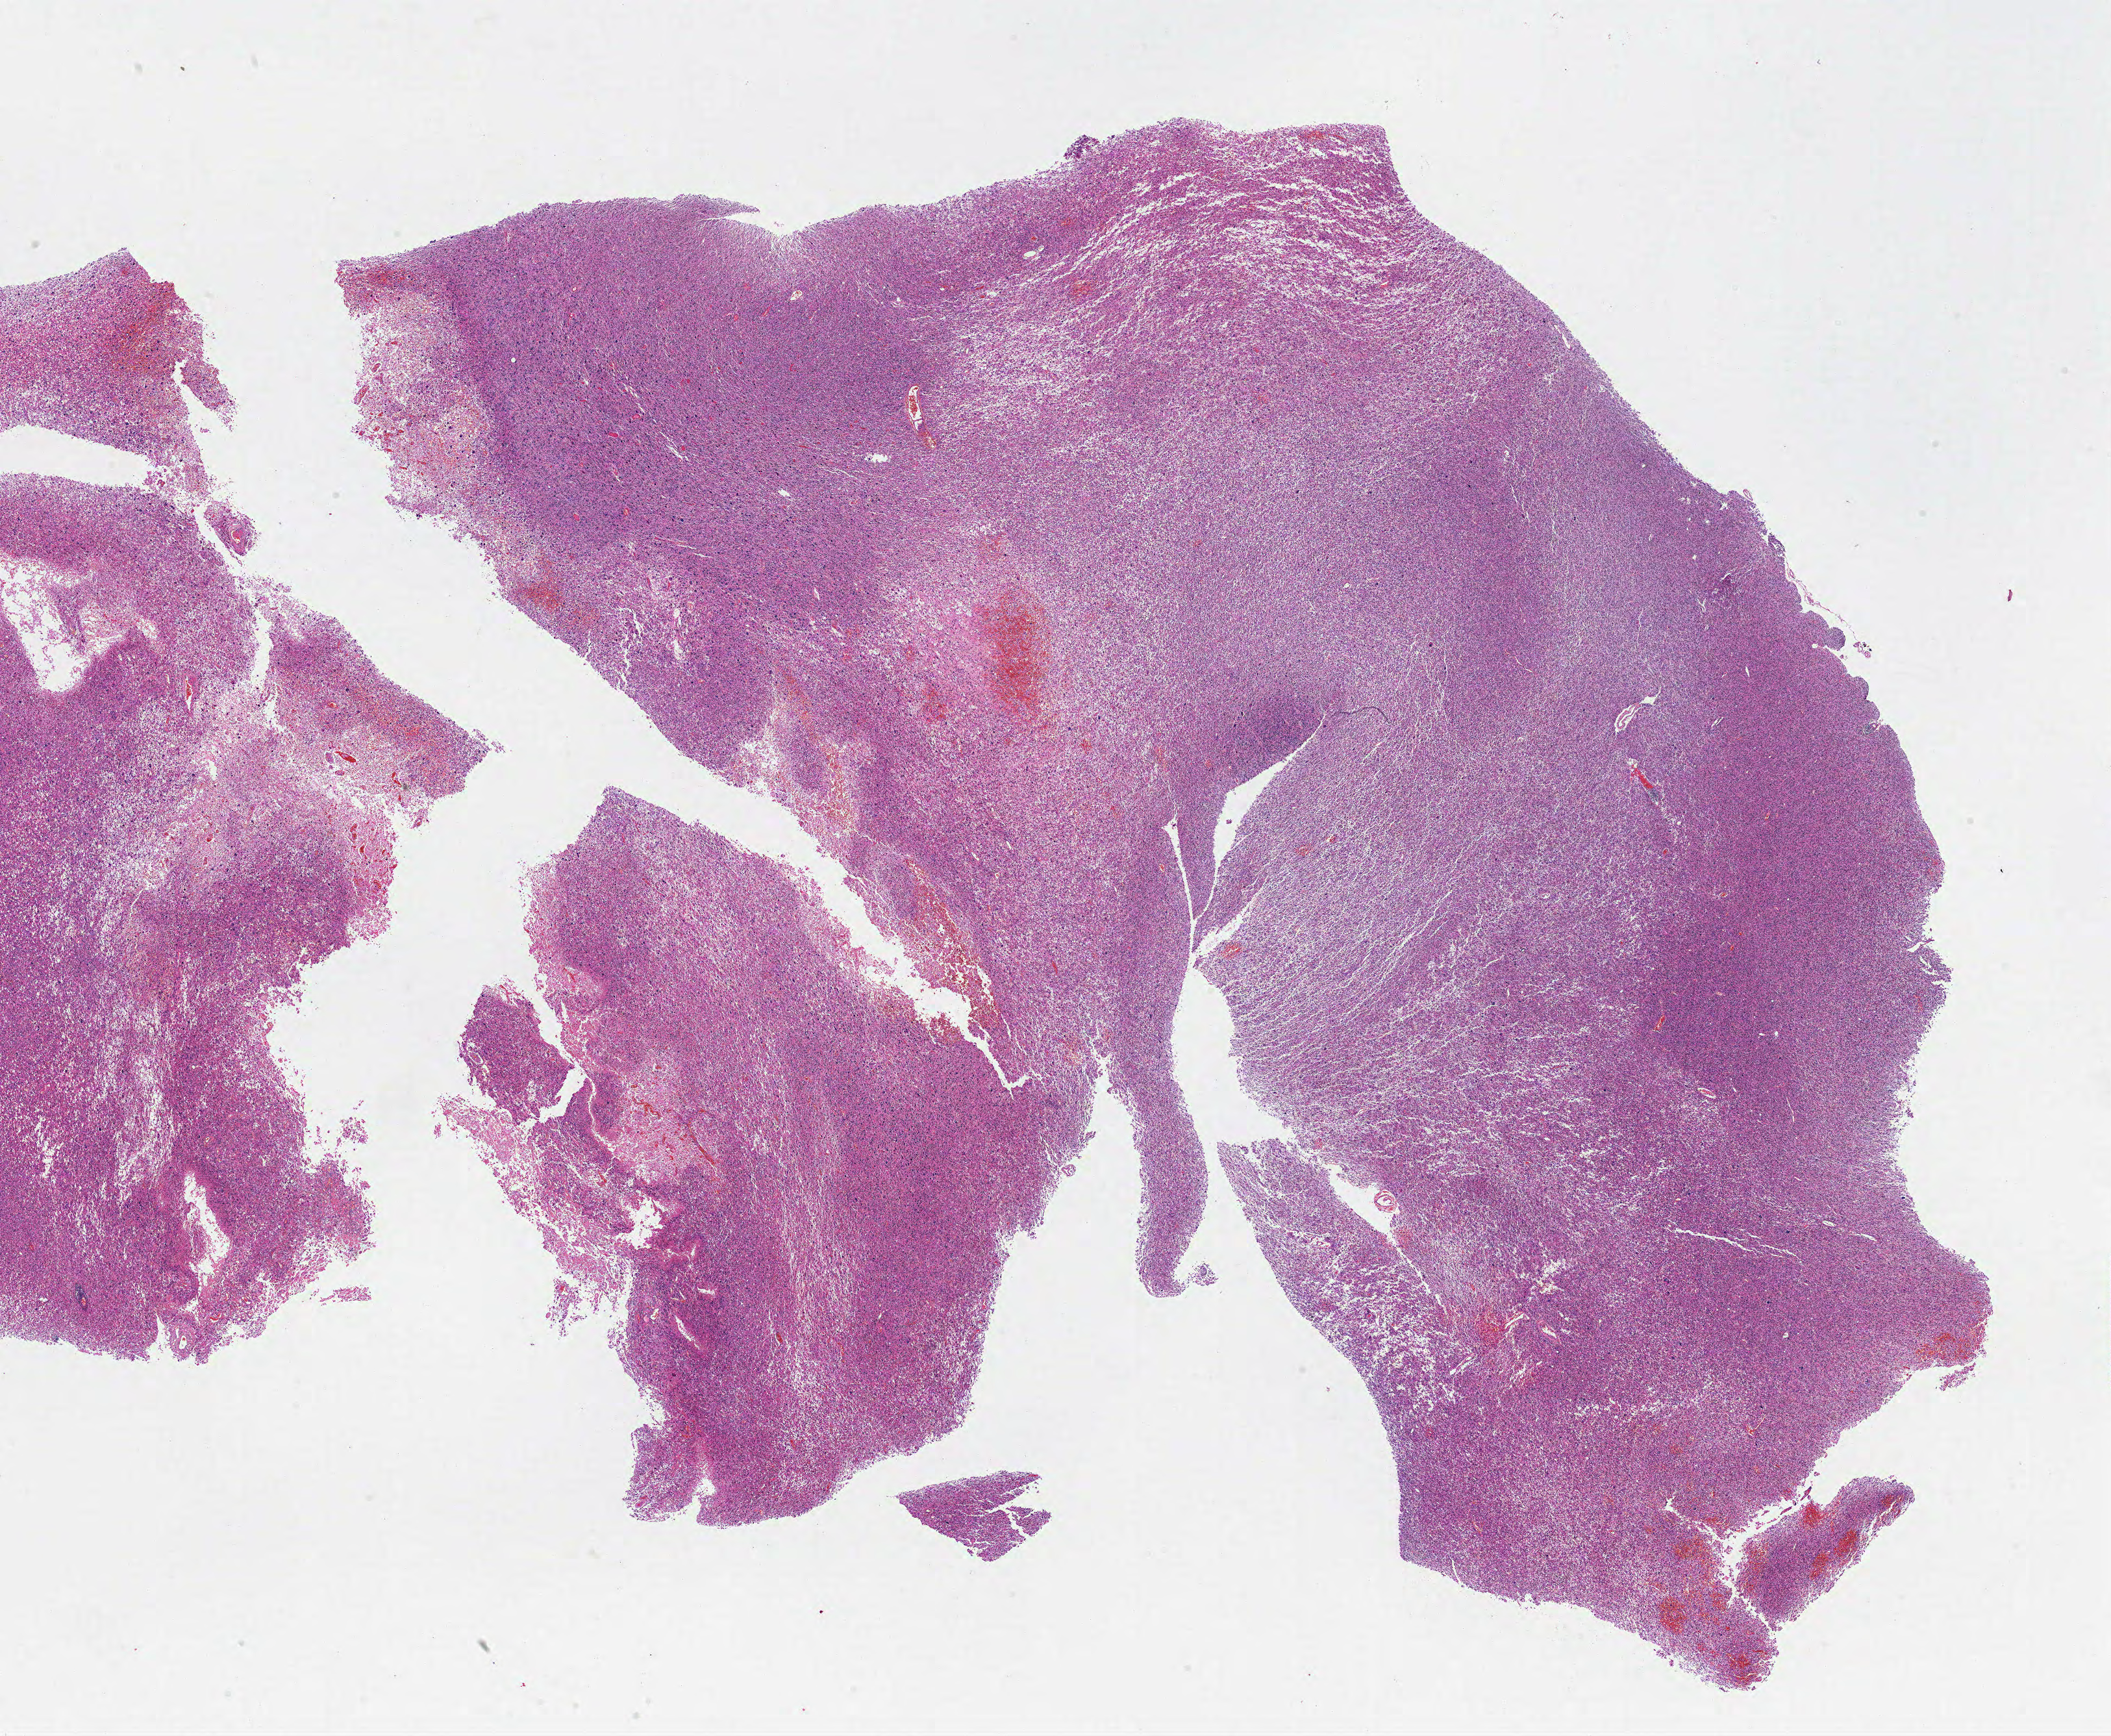
Whole-slide histology image, H&E-stained — shown as a low-resolution overview of the whole scanned area (about 26.0 x 21.4 mm); formalin-fixed paraffin-embedded (FFPE) diagnostic section; primary tumour sample from the brain. Patient: male, age at initial diagnosis 63 years.
• diagnosis: Glioblastoma